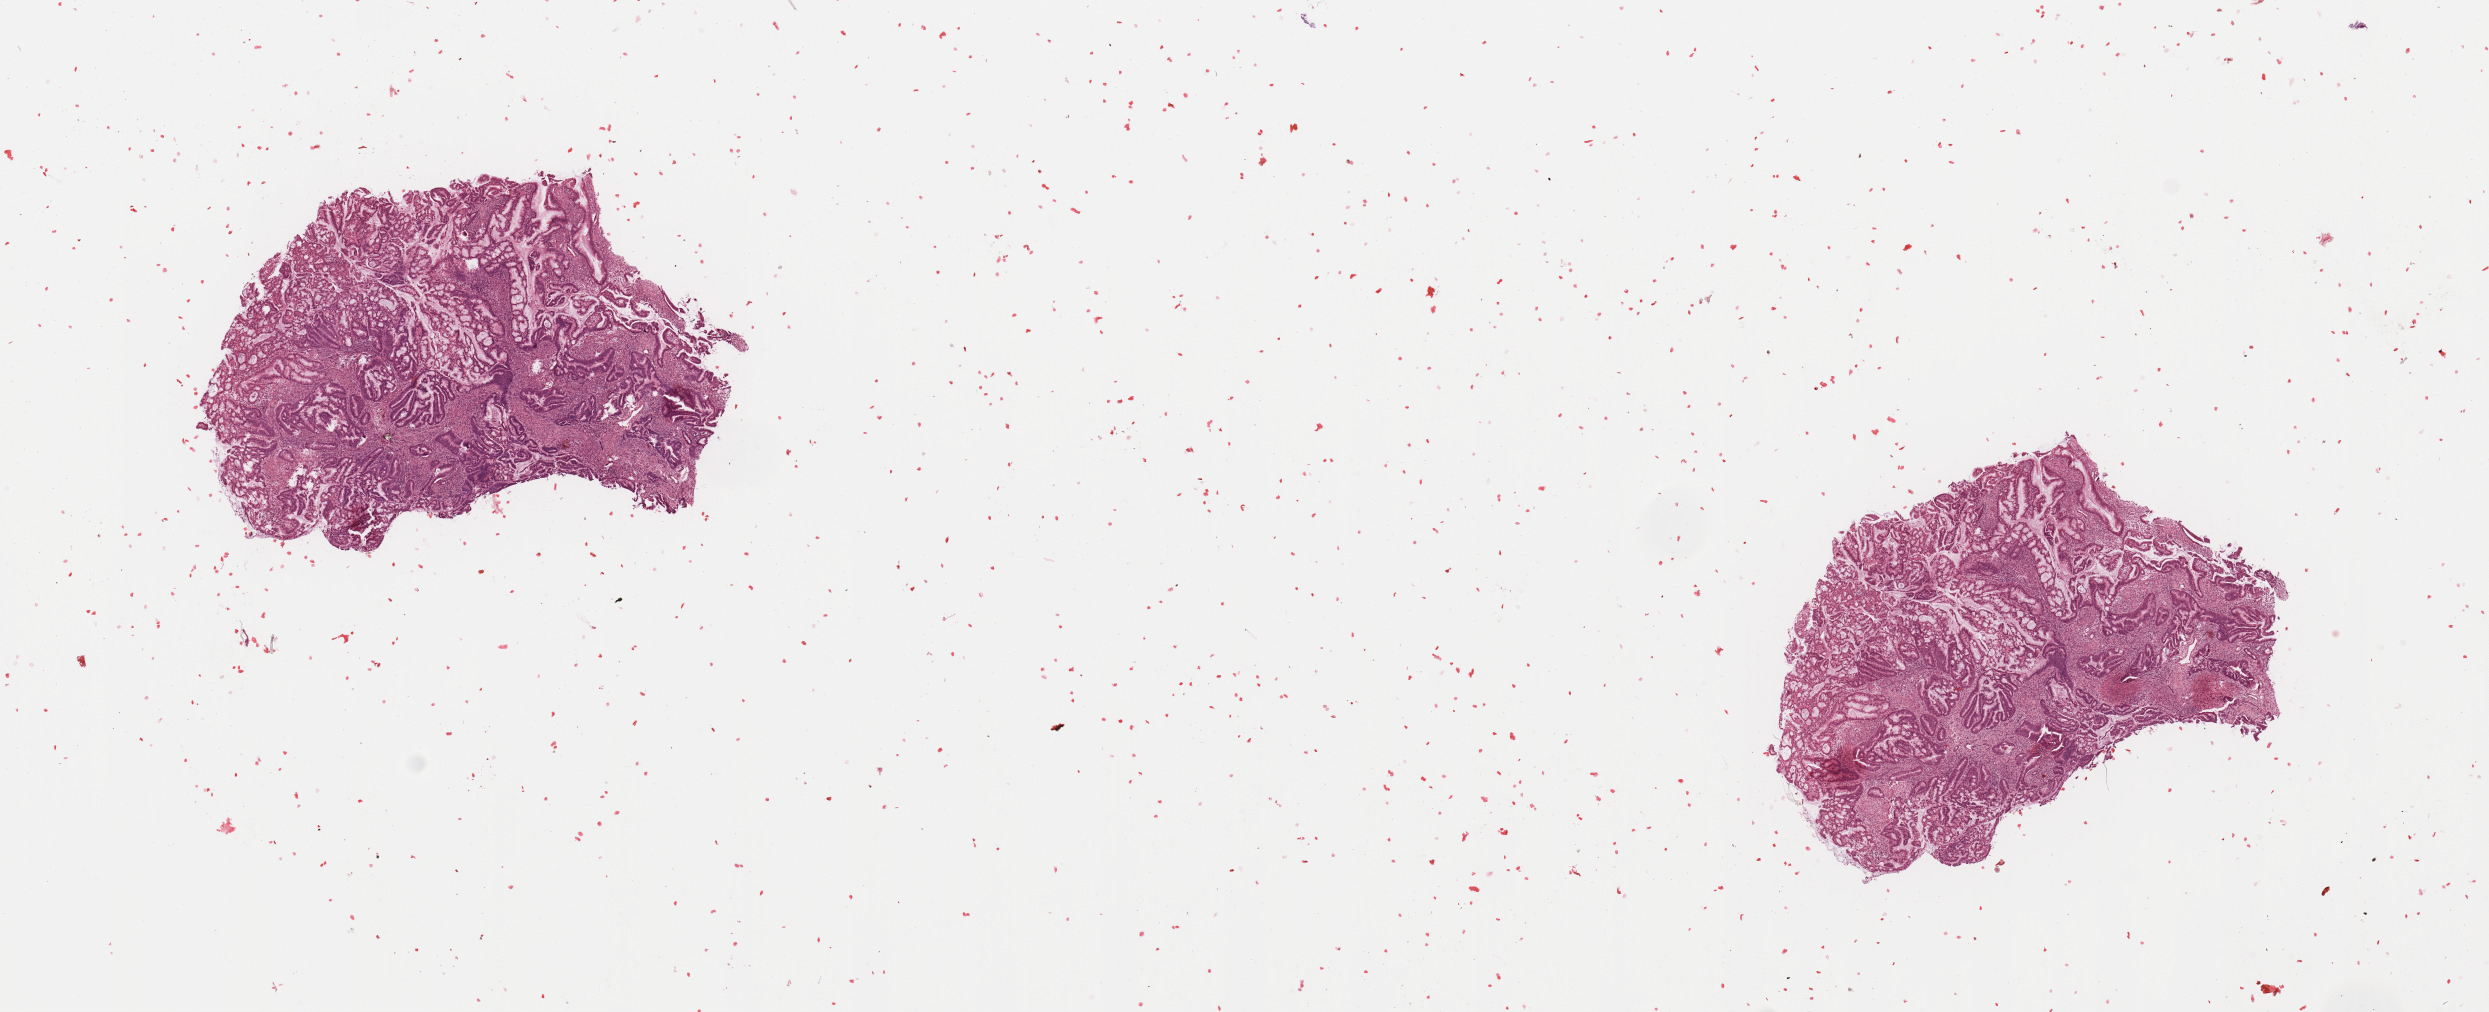
Whole-slide histology image, Hematoxylin and eosin (H&E) stained — low-resolution overview of the scanned area, about 19.7 x 8.0 mm (slide scanned at 20x). Tumour tissue sample, sampled site: uterus. Female, 83 y/o. Histologic grade: G1 (well differentiated). Composition of this section per pathologist review: tumour nuclei 80%, necrosis 2%.
Primary tumour site (as recorded): posterior endometrium. Histologic diagnosis: Endometrioid adenocarcinoma, NOS. AJCC pathologic stage: I.